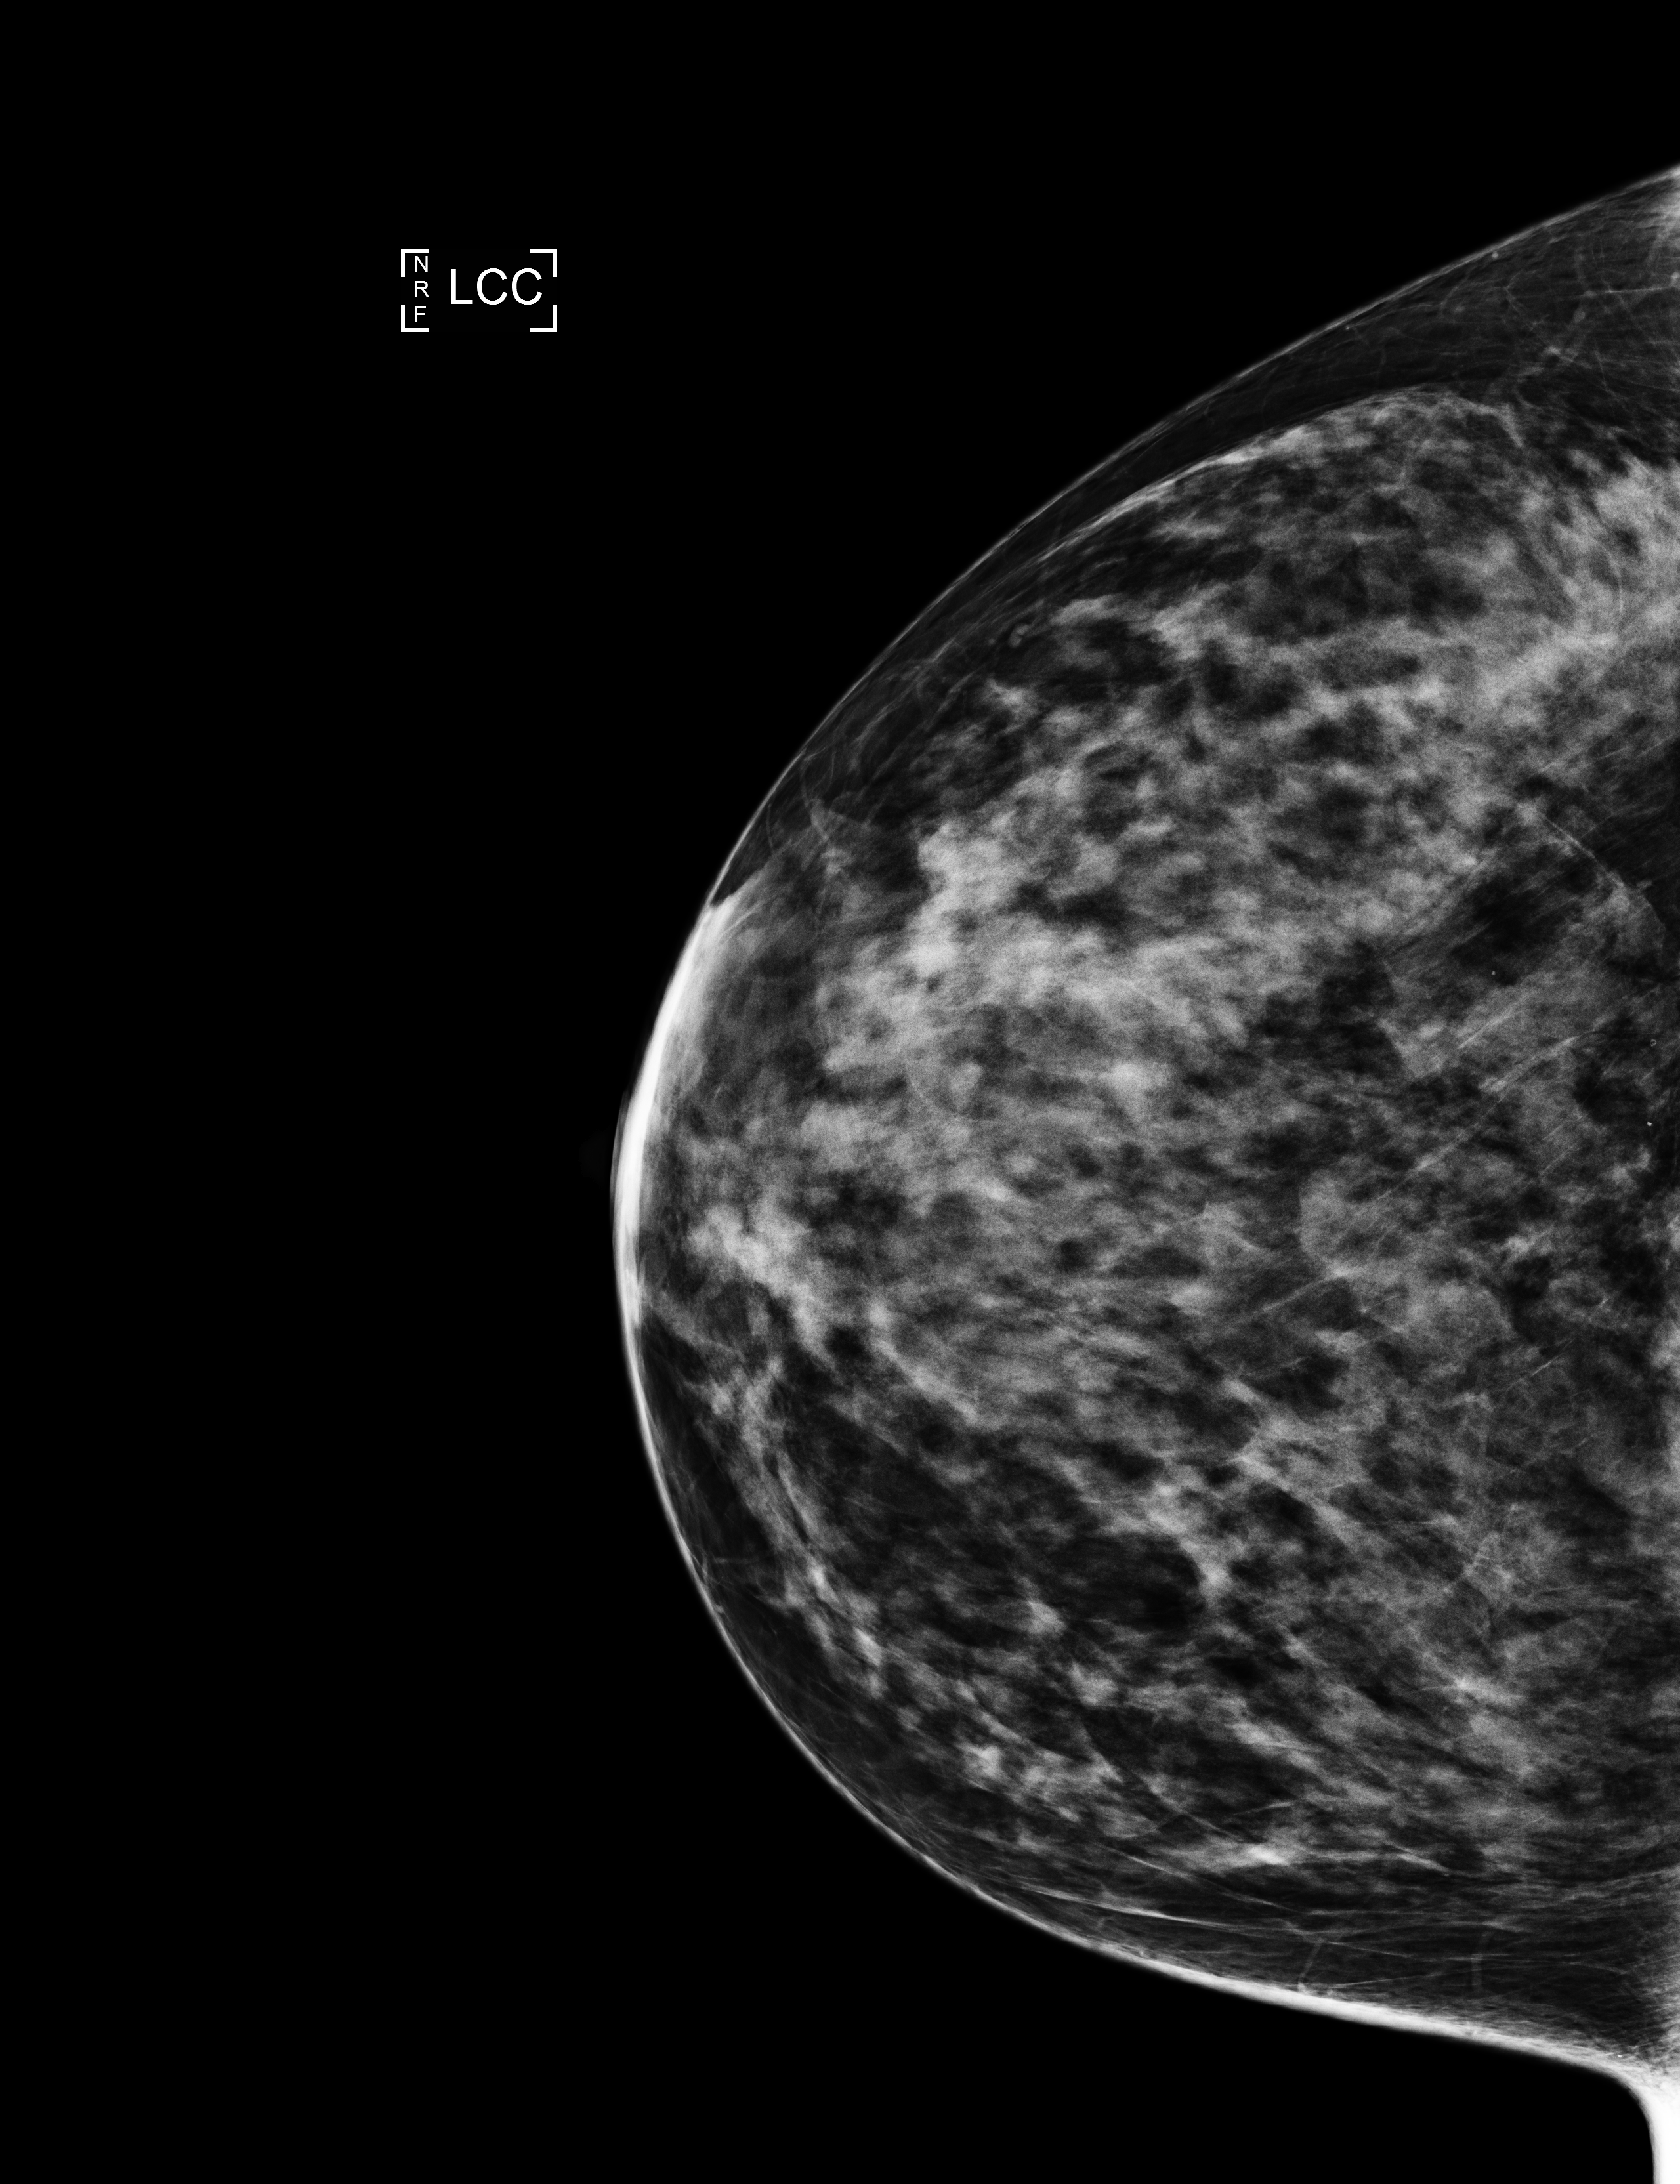
Screening examination, compressed breast thickness 67 mm. Patient: female, 60 years.
Image type: full-field digital mammogram. Breast: left. Projection: craniocaudal (CC) view.